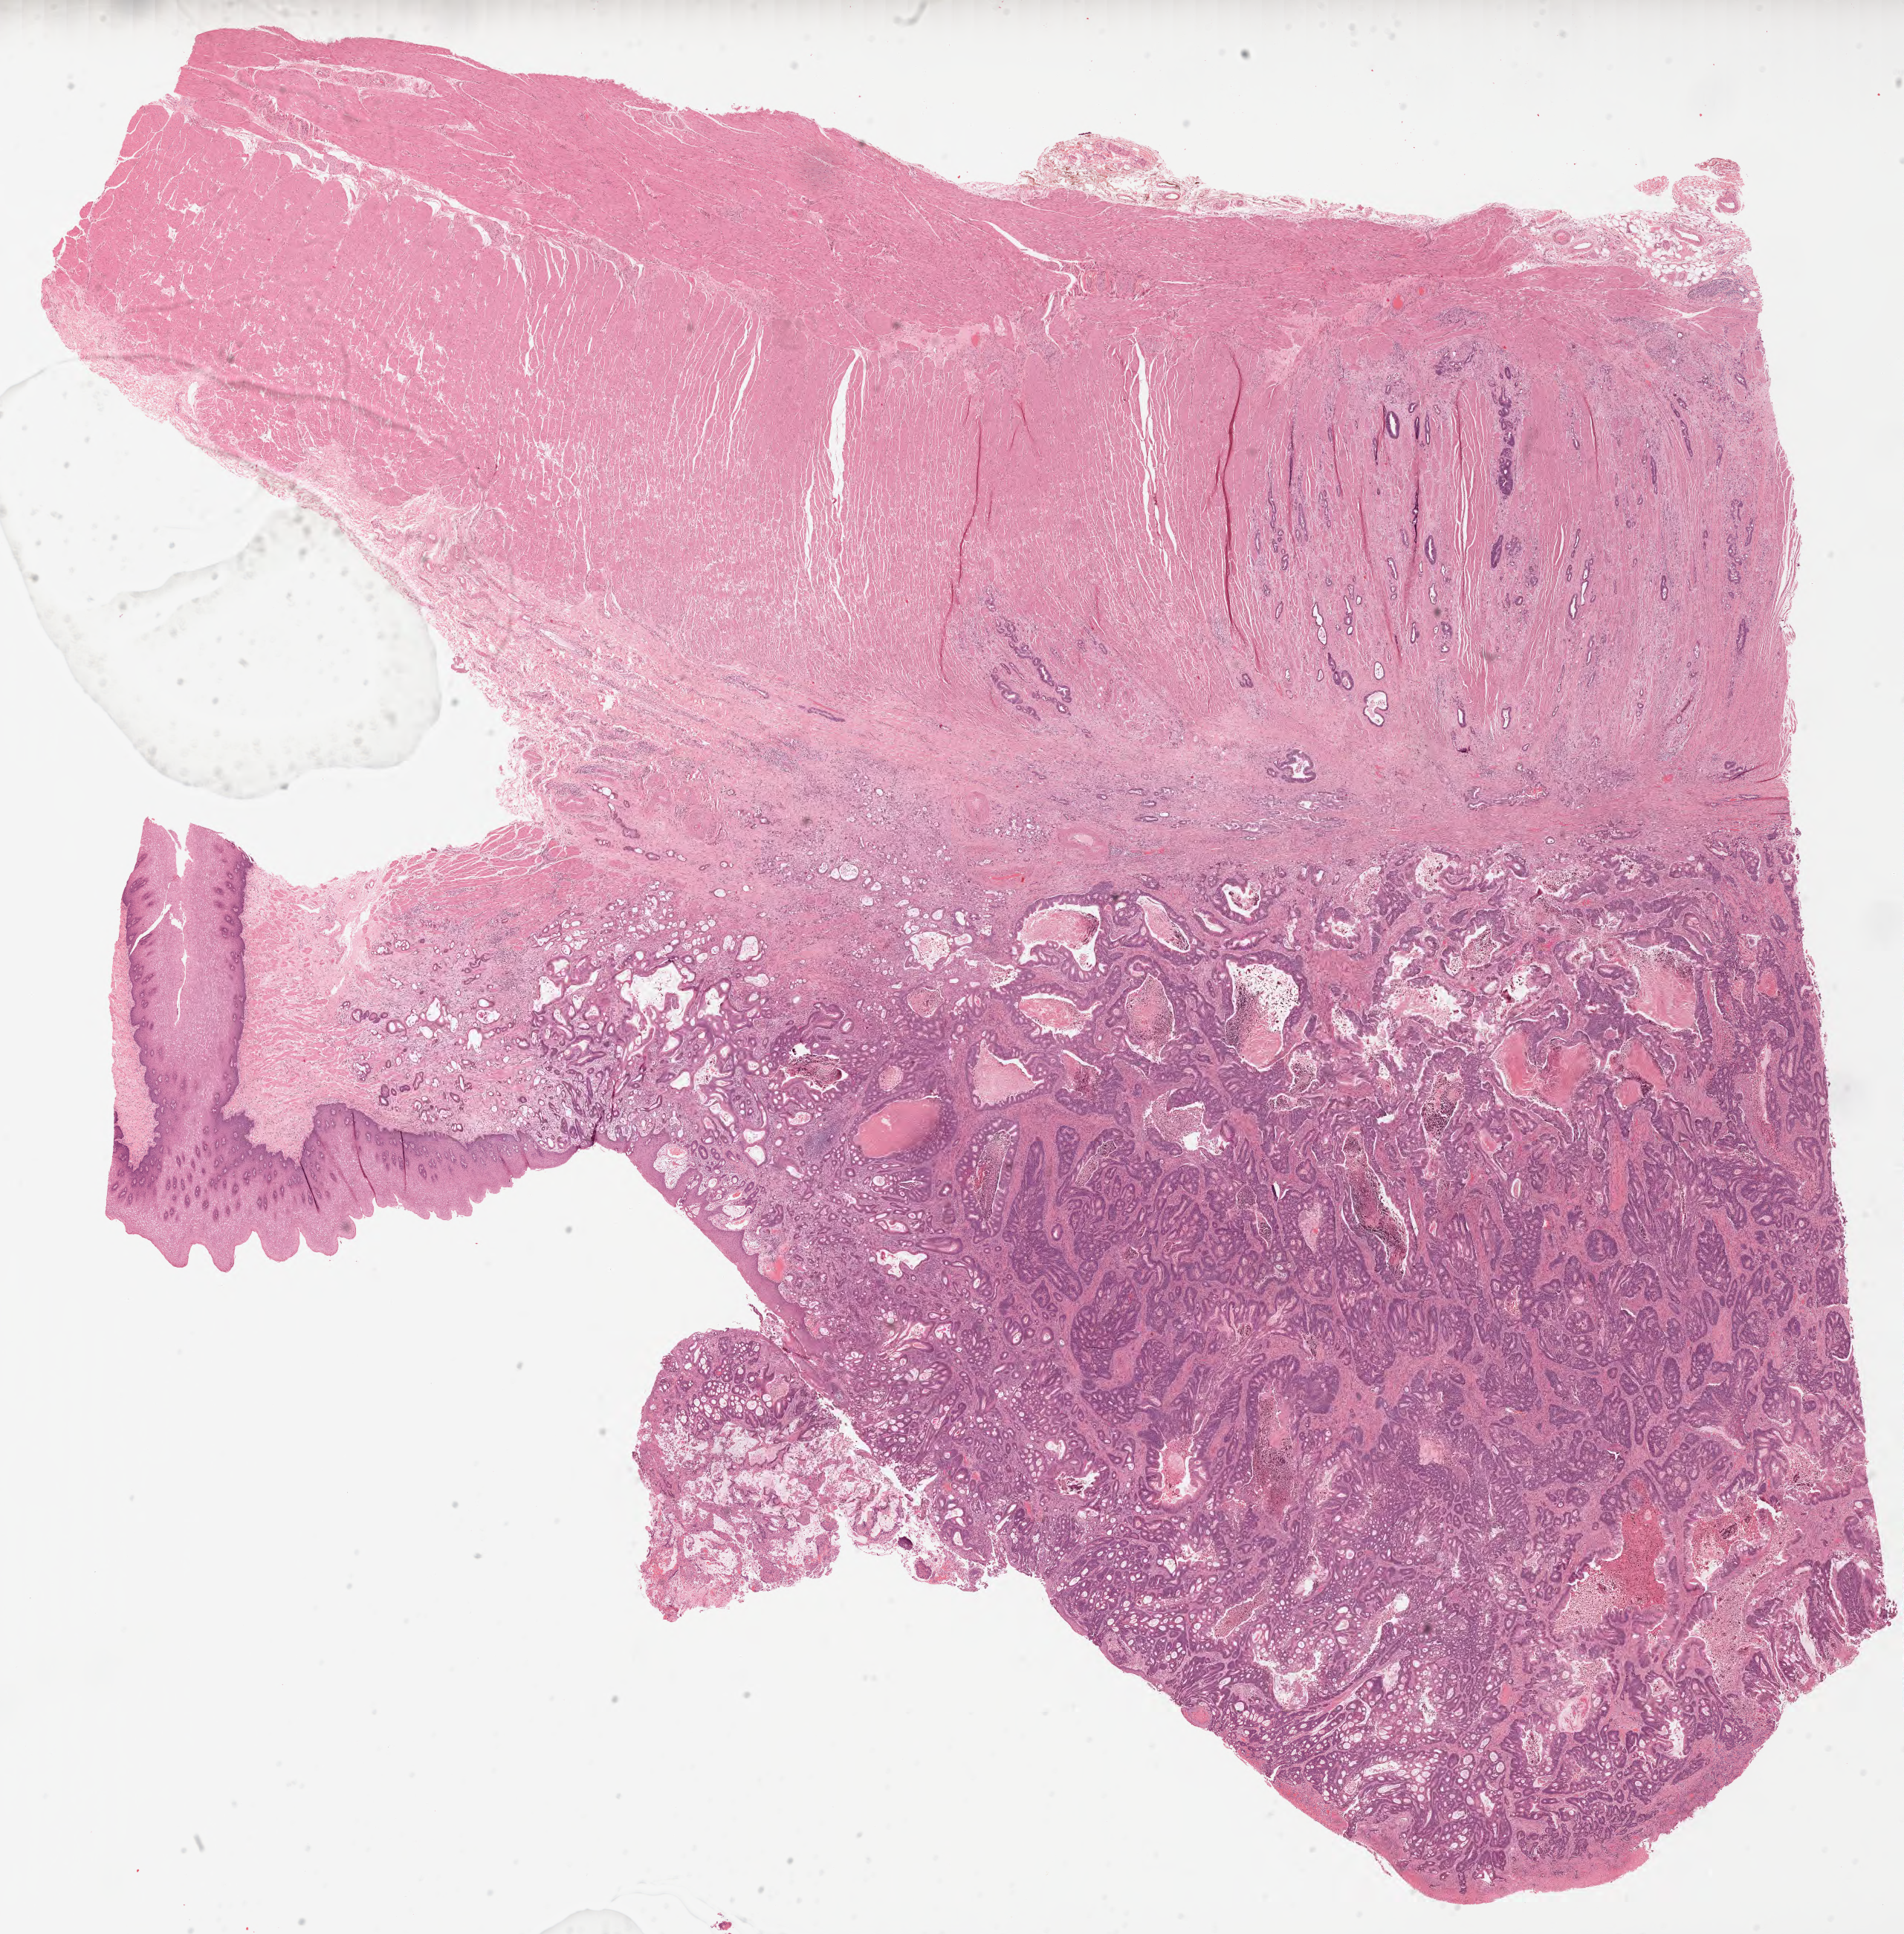
Digitized H&E-stained tissue section (whole slide), shown as a low-resolution overview of the whole scanned area (about 20.6 x 21.0 mm); formalin-fixed paraffin-embedded (FFPE) diagnostic section; sample: primary tumour, esophagus. Patient: male, age at initial diagnosis 47 years. Histologic grade: G3 (poorly differentiated).
* AJCC pathologic stage: IIIB
* TNM: T3 N2 M0
* lymph nodes positive (case pathology): 3 of 17 examined
* diagnosis: Adenocarcinoma, NOS (lower third of esophagus)